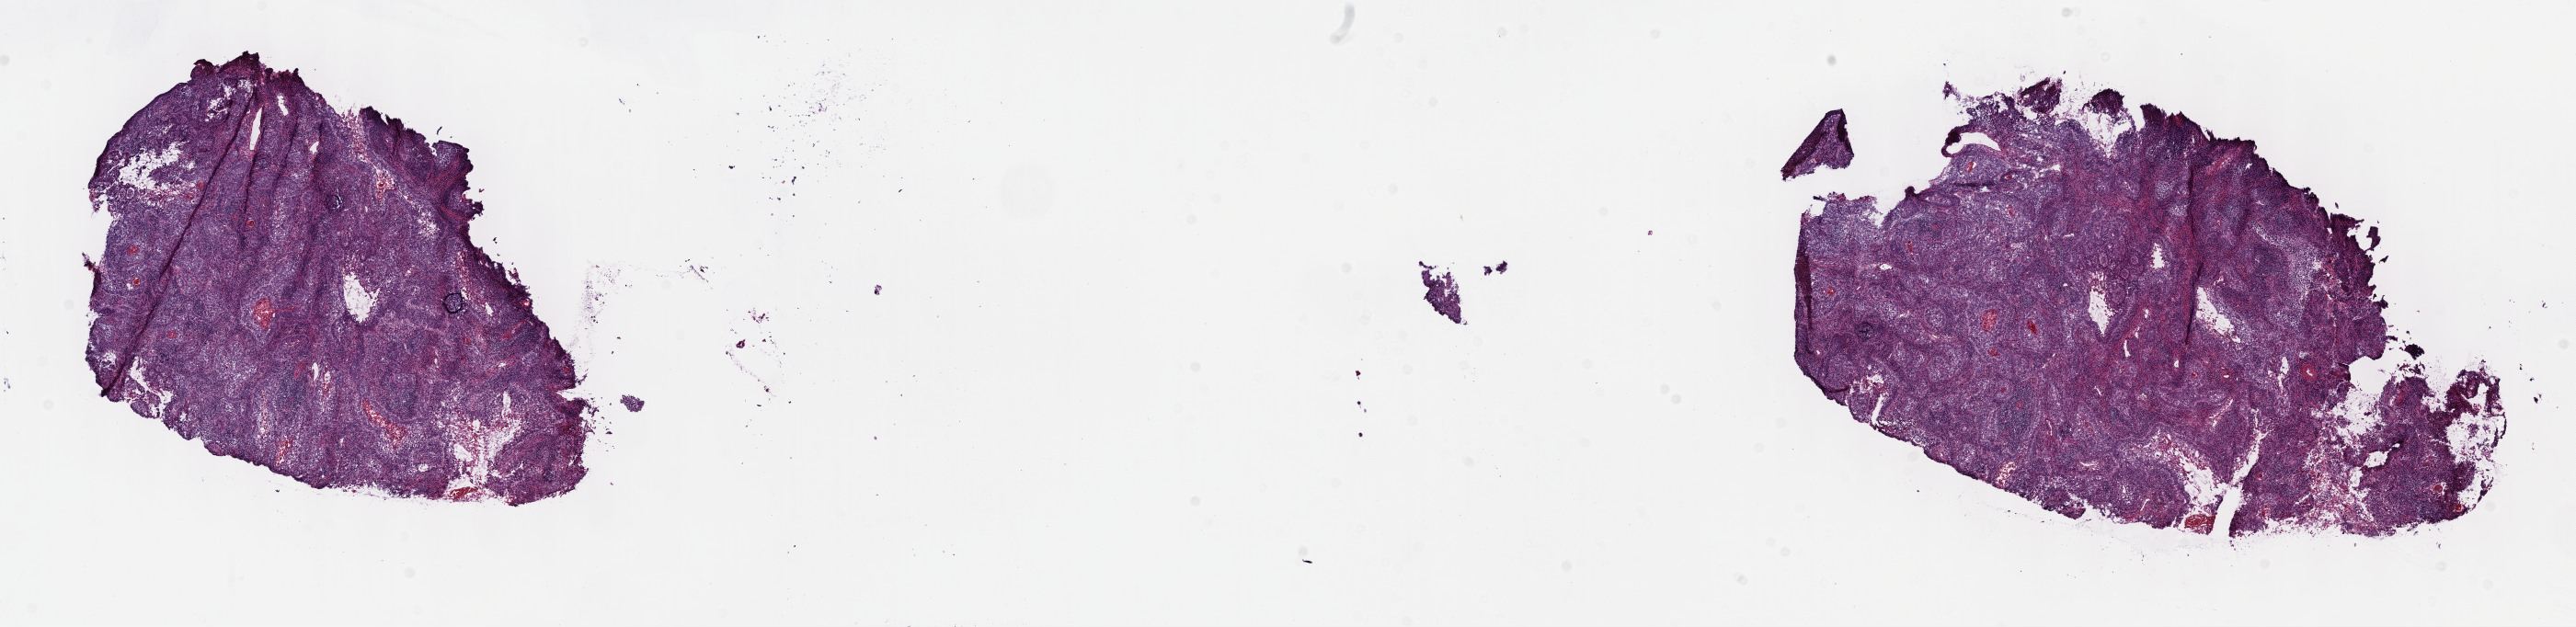
Whole-slide histology image, H&E — shown as a low-resolution overview of the whole scanned area (about 22.7 x 5.5 mm, from a 40x scan); frozen section from the top of the tissue portion; sample: primary tumour, cervix. Female patient; age at initial diagnosis 38 years. Histologic grade: GX (grade cannot be assessed). Composition of this section per pathologist review: tumour cells 60%, tumour nuclei 60%, normal cells 5%, stromal cells 35%, necrosis 0%. Infiltration values recorded for this section: lymphocyte infiltration 20%, monocyte infiltration 0%, neutrophil infiltration 0%.
Diagnosis: Squamous cell carcinoma, NOS (cervix uteri). FIGO stage: IIB.